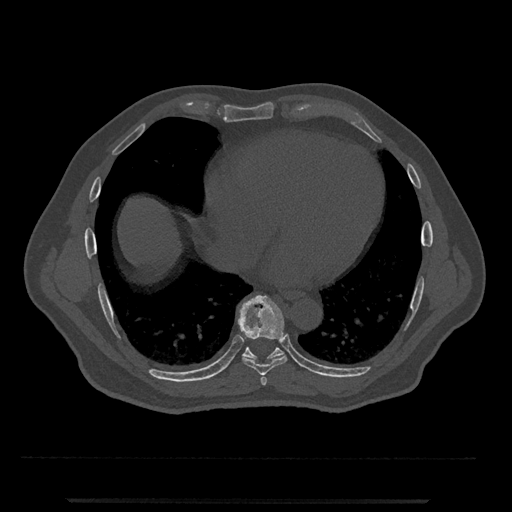
CT including the spine, one axial slice; position 608 of 797 along the scan axis; reconstruction kernel Br40s/3; 120 kVp; bone window (W 1800 / L 400 HU); 512 × 512 image matrix, field of view 419 × 419 mm. Male patient, age 63 years. From the clinical record (not read from this slice): primary cancer: prostate.
Annotated regions visible in this slice (semi-automatically segmented with operator editing):
- T7 vertebra: bounding box (x1, y1, x2, y2) in pixels: (260, 375, 267, 385)
- T8 vertebra: (238, 295, 287, 375)
- T9 vertebra: (225, 346, 284, 369)